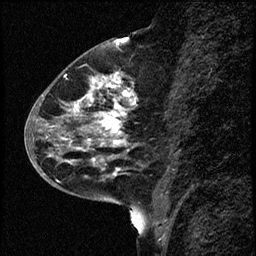
Breast MRI (dynamic contrast-enhanced), one sagittal slice; slice 27 of 68 in the series (ordered by position); dynamic contrast-enhanced study with each time point stored as its own series, time point 2 of 3 at this slice position (early post-contrast, ordered by acquisition time); 1.5 T; TE 4.2 ms, TR 17.6 ms; 2 mm slice thickness; 256 × 256 image matrix, field of view 200 × 200 mm. Patient: female, 52 years. Case-level facts recorded for this patient, not image findings: setting: breast cancer imaged before/during neoadjuvant chemotherapy; receptor status: HER2-positive.
Annotated regions visible in this slice (semi-automatic segmentation, software-assisted and operator-edited):
- analysis volume of interest (the breast-tissue region the enhancement analysis was run in; not a lesion): box from (x=50, y=61) to (x=150, y=184) px
- tumour enhancement mask (voxels above the 100 % enhancement threshold inside the analysis volume of interest): (x=60, y=73)–(x=134, y=164)